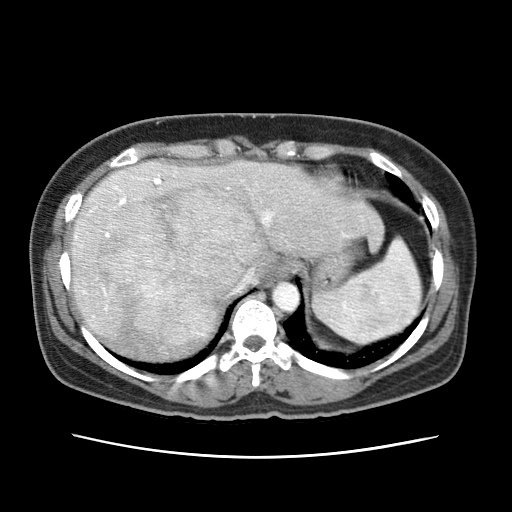
Contrast-enhanced abdominal CT (liver protocol), one axial slice; slice 54 of 79 in the series (ordered by position); 120 kVp; soft-tissue window (W 400 / L 40 HU); 2.5 mm slice thickness; 512 × 512 image matrix, field of view 340 × 340 mm. From the clinical record (not read from this slice): diagnosis: hepatocellular carcinoma (patient treated with transarterial chemoembolisation; whether this scan precedes or follows treatment is not stated here); TNM stage (as recorded): Stage-I; Child-Pugh class: A; tumour differentiation: moderately differentiated.
Outlined on this slice (semi-automatic segmentation, software-assisted and operator-edited):
- abdominal aorta: bounding box (x1, y1, x2, y2) in pixels: (272, 282, 299, 312)
- liver parenchyma outside the tumour (the mass and vessels are separate outlines, so this box may not span the whole liver): (70, 160, 373, 358)
- mass: (100, 180, 265, 345)
- liver vessels: (75, 177, 345, 317)